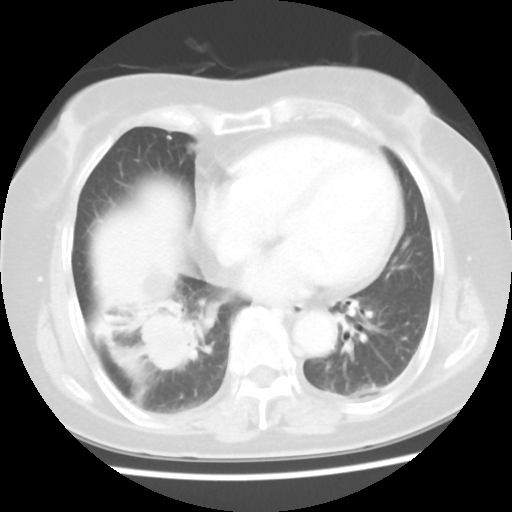
Chest CT, one axial slice; slice 16 of 45 in the series (ordered by position); reconstruction kernel STANDARD; 120 kVp; lung window (W 1500 / L -600 HU); 5 mm slice thickness; 512 × 512 image matrix, field of view 312 × 312 mm. Female patient, age 65 years. From the clinical record (not read from this slice): clinical TNM (as recorded): T2 N3 M0.
Structures marked on this image (bounding box drawn by a radiologist):
- lung tumour (recorded histology: adenocarcinoma): bounding box <127,296,201,383> (left, top, right, bottom; pixels)